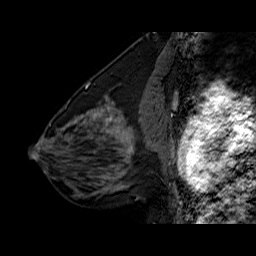
Breast MRI (dynamic contrast-enhanced), one sagittal slice; position 28 of 60 along the scan axis; dynamic contrast-enhanced series, time point 2 of 6 at this slice position (early post-contrast); 1.5 T; TE 6.3 ms, TR 32.5 ms; 4 mm slice thickness; 256 × 256 image matrix, field of view 200 × 200 mm. Female patient. From the clinical record (not read from this slice): setting: breast cancer imaged before/during neoadjuvant chemotherapy; receptor status: triple-negative.
Structures marked on this image (semi-automatically segmented with operator editing):
- analysis volume of interest (the breast-tissue region the enhancement analysis was run in; not a lesion): bounding box <108,126,154,177> (left, top, right, bottom; pixels)
- tumour enhancement mask (voxels above the 100 % enhancement threshold inside the analysis volume of interest): <115,129,133,153>